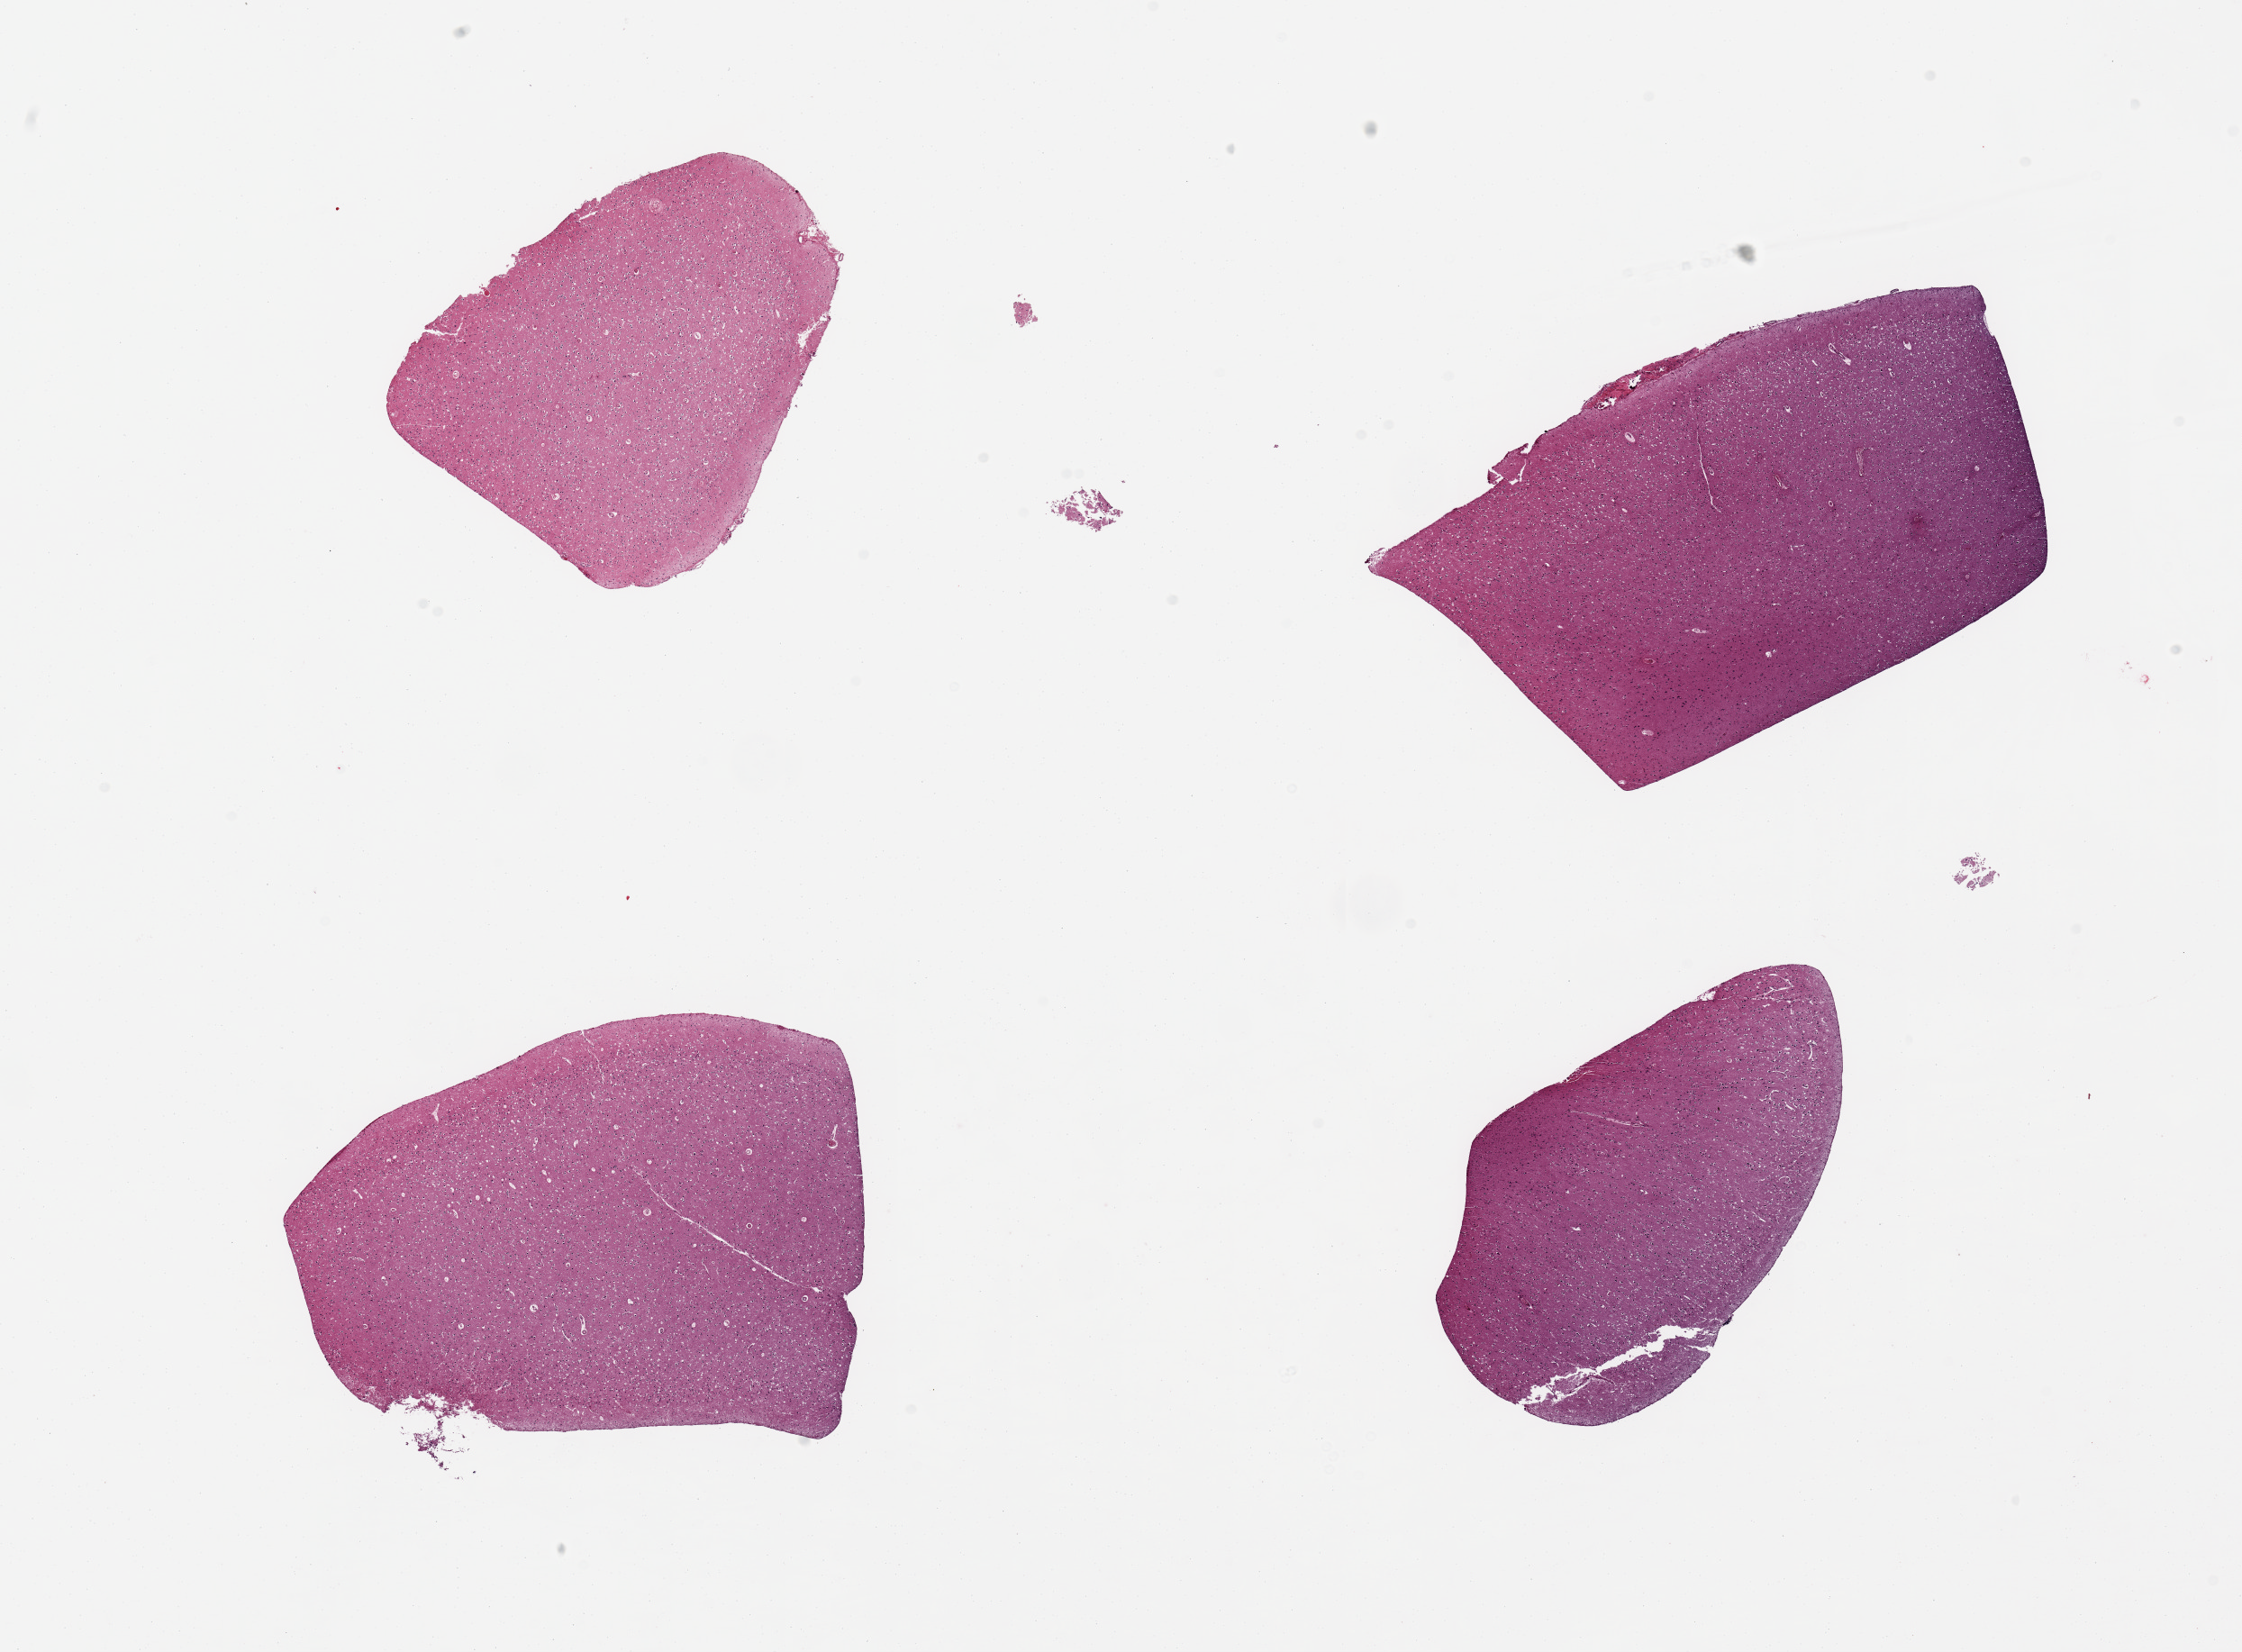
Whole-slide image, hematoxylin and eosin (H&E) stain — a low-resolution overview of the entire scanned area, about 19.7 x 14.5 mm, PAXgene-fixed, paraffin-embedded tissue, sampled site (target tissue): cerebral cortex, donor tissue sample. Donor: male.
Review note (as recorded): 4 pieces.